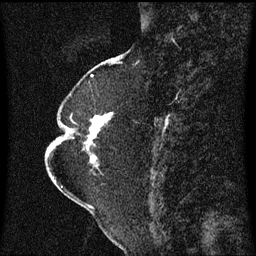
Breast MRI (dynamic contrast-enhanced), one sagittal slice. Slice 24 of 60 in the series (ordered by position). Dynamic contrast-enhanced series, image 2 of 3 at this slice position (ordered by acquisition). 1.5 T. TE 4.2 ms, TR 8.4 ms. 2 mm slice thickness. 256 × 256 image matrix, field of view 200 × 200 mm. Patient: female, 52 years. From the clinical record (not read from this slice): setting: breast cancer imaged before/during neoadjuvant chemotherapy; receptor status: HR-positive, HER2-negative.
Annotated regions visible in this slice (semi-automatic segmentation, software-assisted and operator-edited):
- analysis volume of interest (the breast-tissue region the enhancement analysis was run in; not a lesion): bounding box (x1, y1, x2, y2) in pixels: (64, 104, 115, 167)
- tumour enhancement mask (voxels above the 70 % enhancement threshold inside the analysis volume of interest): (86, 114, 112, 159)